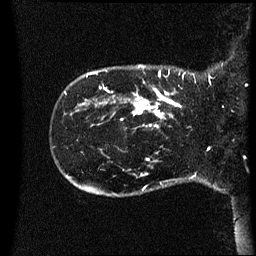
Breast MRI (dynamic contrast-enhanced), one sagittal slice. Slice 8 of 60 in the series (ordered by position). Dynamic contrast-enhanced series, image 2 of 3 at this slice position (ordered by acquisition). 1.5 T. TE 4.2 ms, TR 8.4 ms. 2.2 mm slice thickness. 256 × 256 image matrix, field of view 220 × 220 mm. Female patient, age 41 years. From the clinical record (not read from this slice): setting: breast cancer imaged before/during neoadjuvant chemotherapy; receptor status: HER2-positive.
Annotated regions visible in this slice (semi-automatic segmentation, software-assisted and operator-edited):
- analysis volume of interest (the breast-tissue region the enhancement analysis was run in; not a lesion): bounding box <122,80,197,123> (left, top, right, bottom; pixels)
- tumour enhancement mask (voxels above the 70 % enhancement threshold inside the analysis volume of interest): <133,88,183,119>